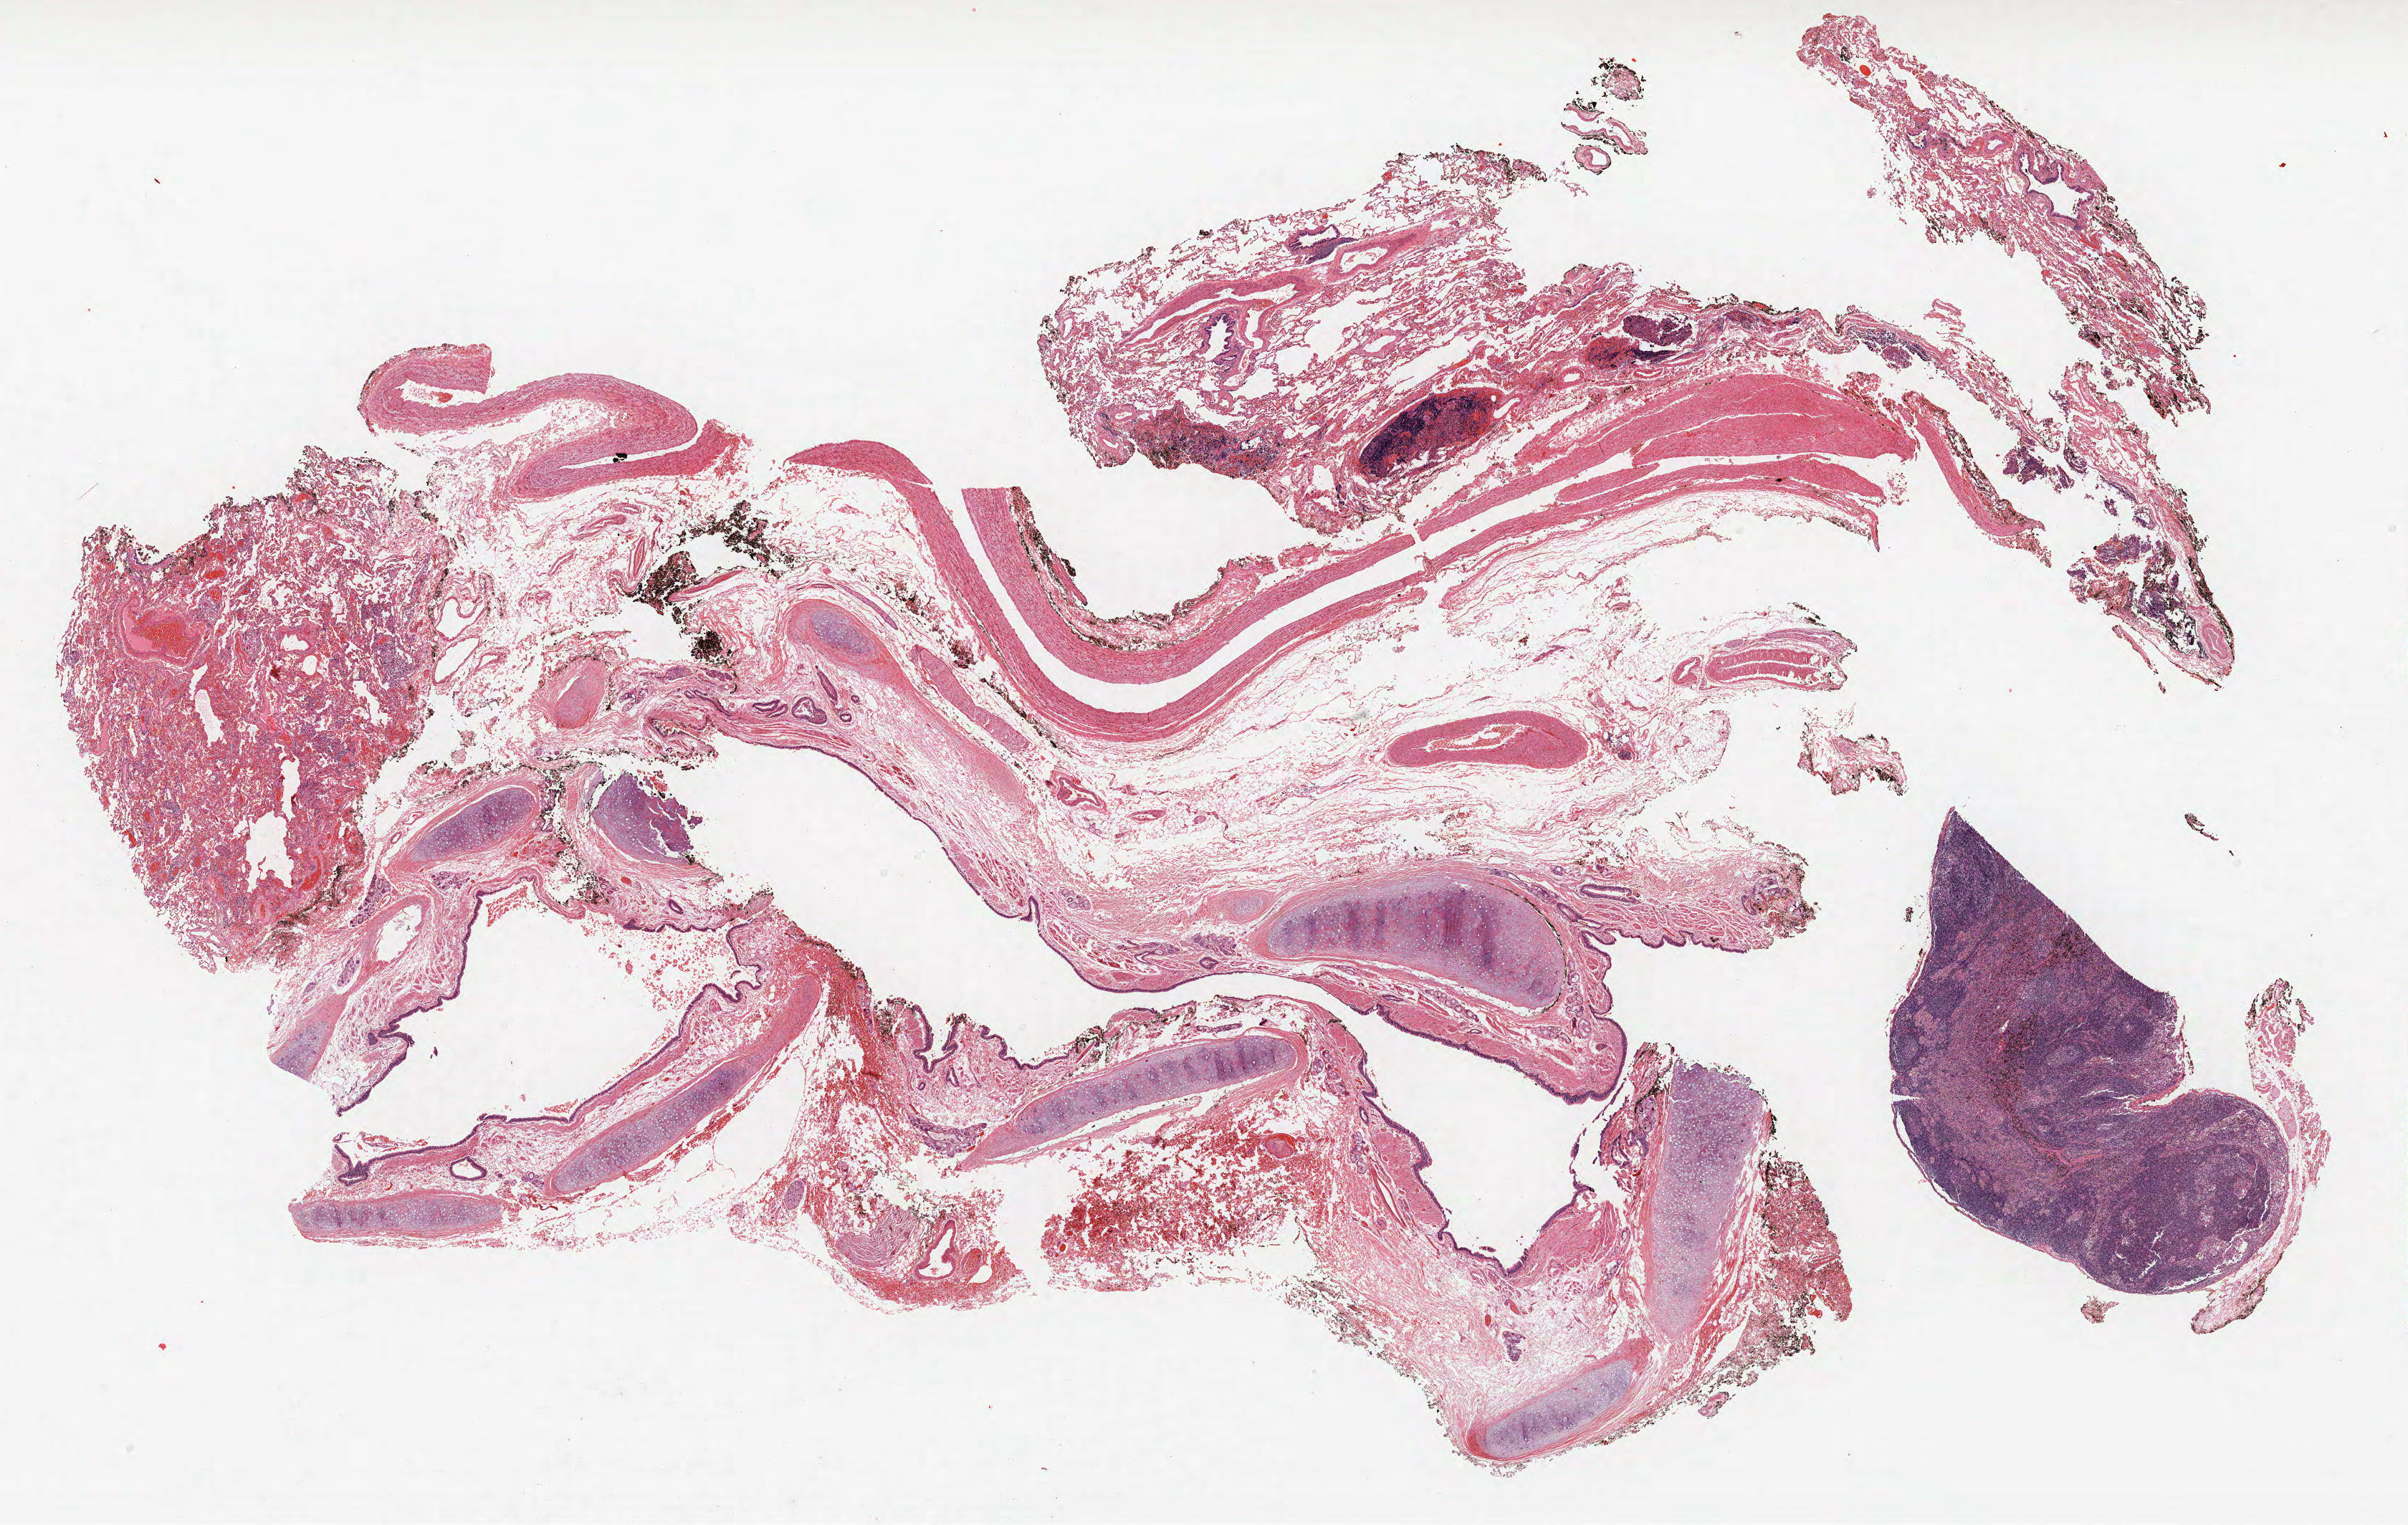
H&E whole-slide image — low-resolution overview of the scanned area, about 26.9 x 17.0 mm. Formalin-fixed paraffin-embedded (FFPE) section. Lung. Female patient, aged 60 at enrolment. Former smoker at enrolment.
Participant's lung-cancer diagnosis: Acinar cell carcinoma (ICD-O-3 8550/3).